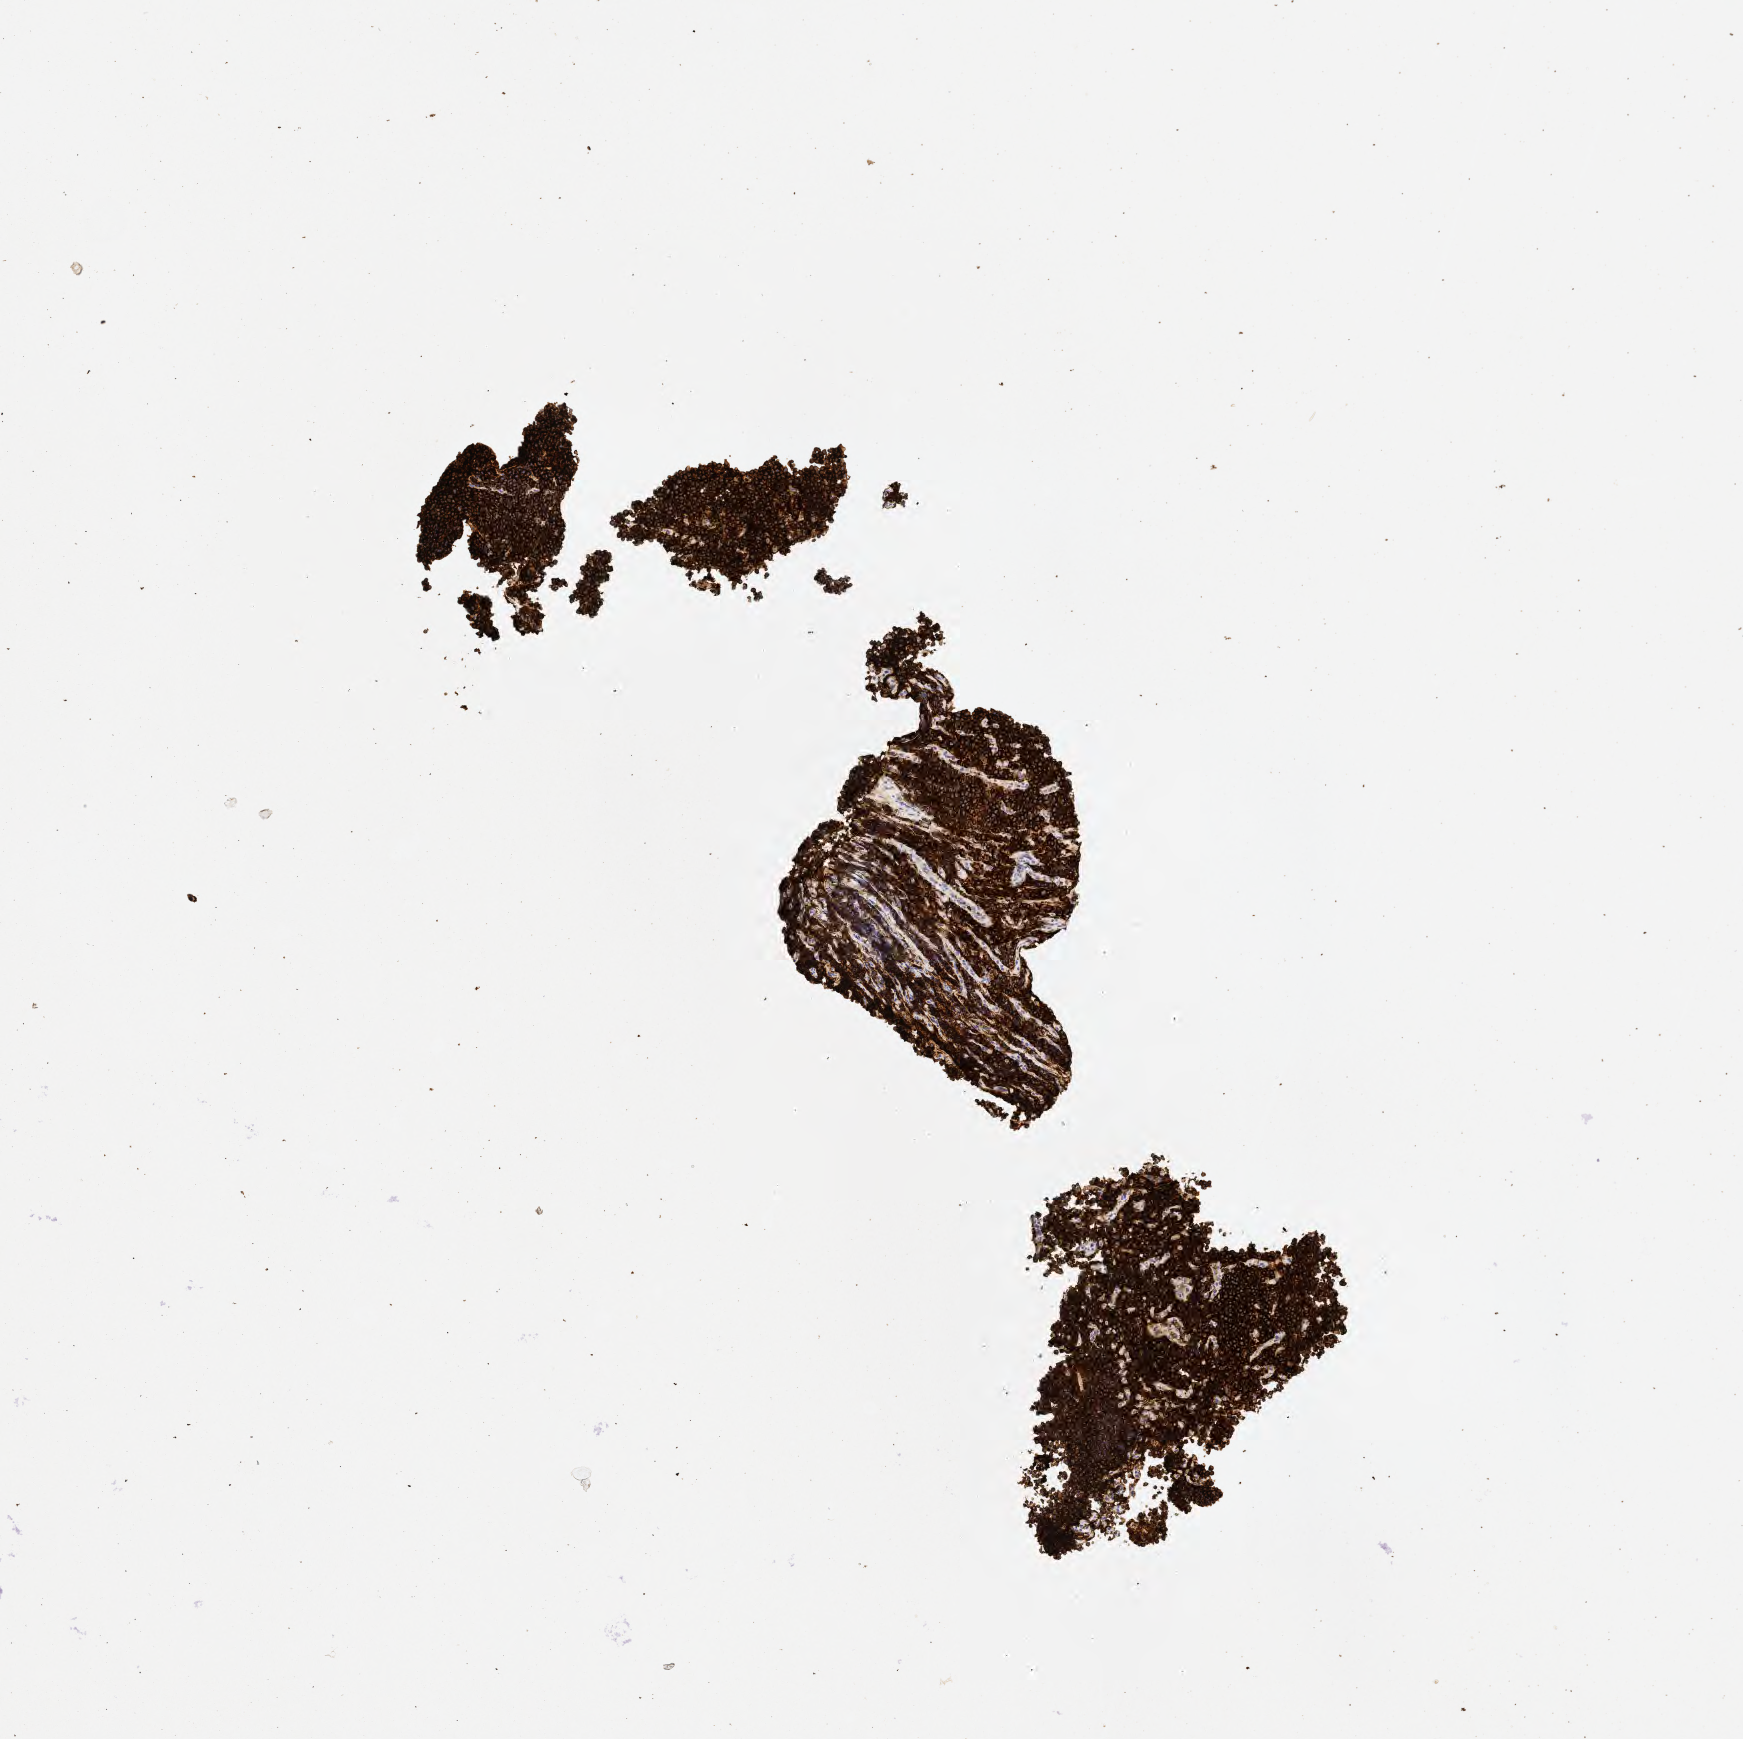
Whole-slide image, immunohistochemical stain for CD20, low-resolution overview of the scanned area, about 3.5 x 3.5 mm, specimen: tumor tissue, site: abdomen proper. Patient: male, age at initial diagnosis 6 years.
Histologic diagnosis: Burkitt lymphoma, NOS.